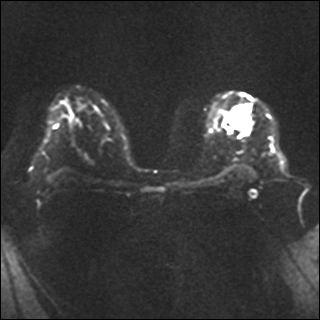
Breast MRI, one axial slice. Position 22 of 35 along the scan axis. Diffusion-weighted series; image 2 of 4 stored at this slice position (different b-values; order by instance number). 1.5 T. 320 × 320 image matrix, field of view 320 × 320 mm. Female patient.
Structures marked on this image (expert manual segmentation):
- tumour on diffusion-weighted imaging: bounding box (x1, y1, x2, y2) in pixels: (230, 107, 240, 128)